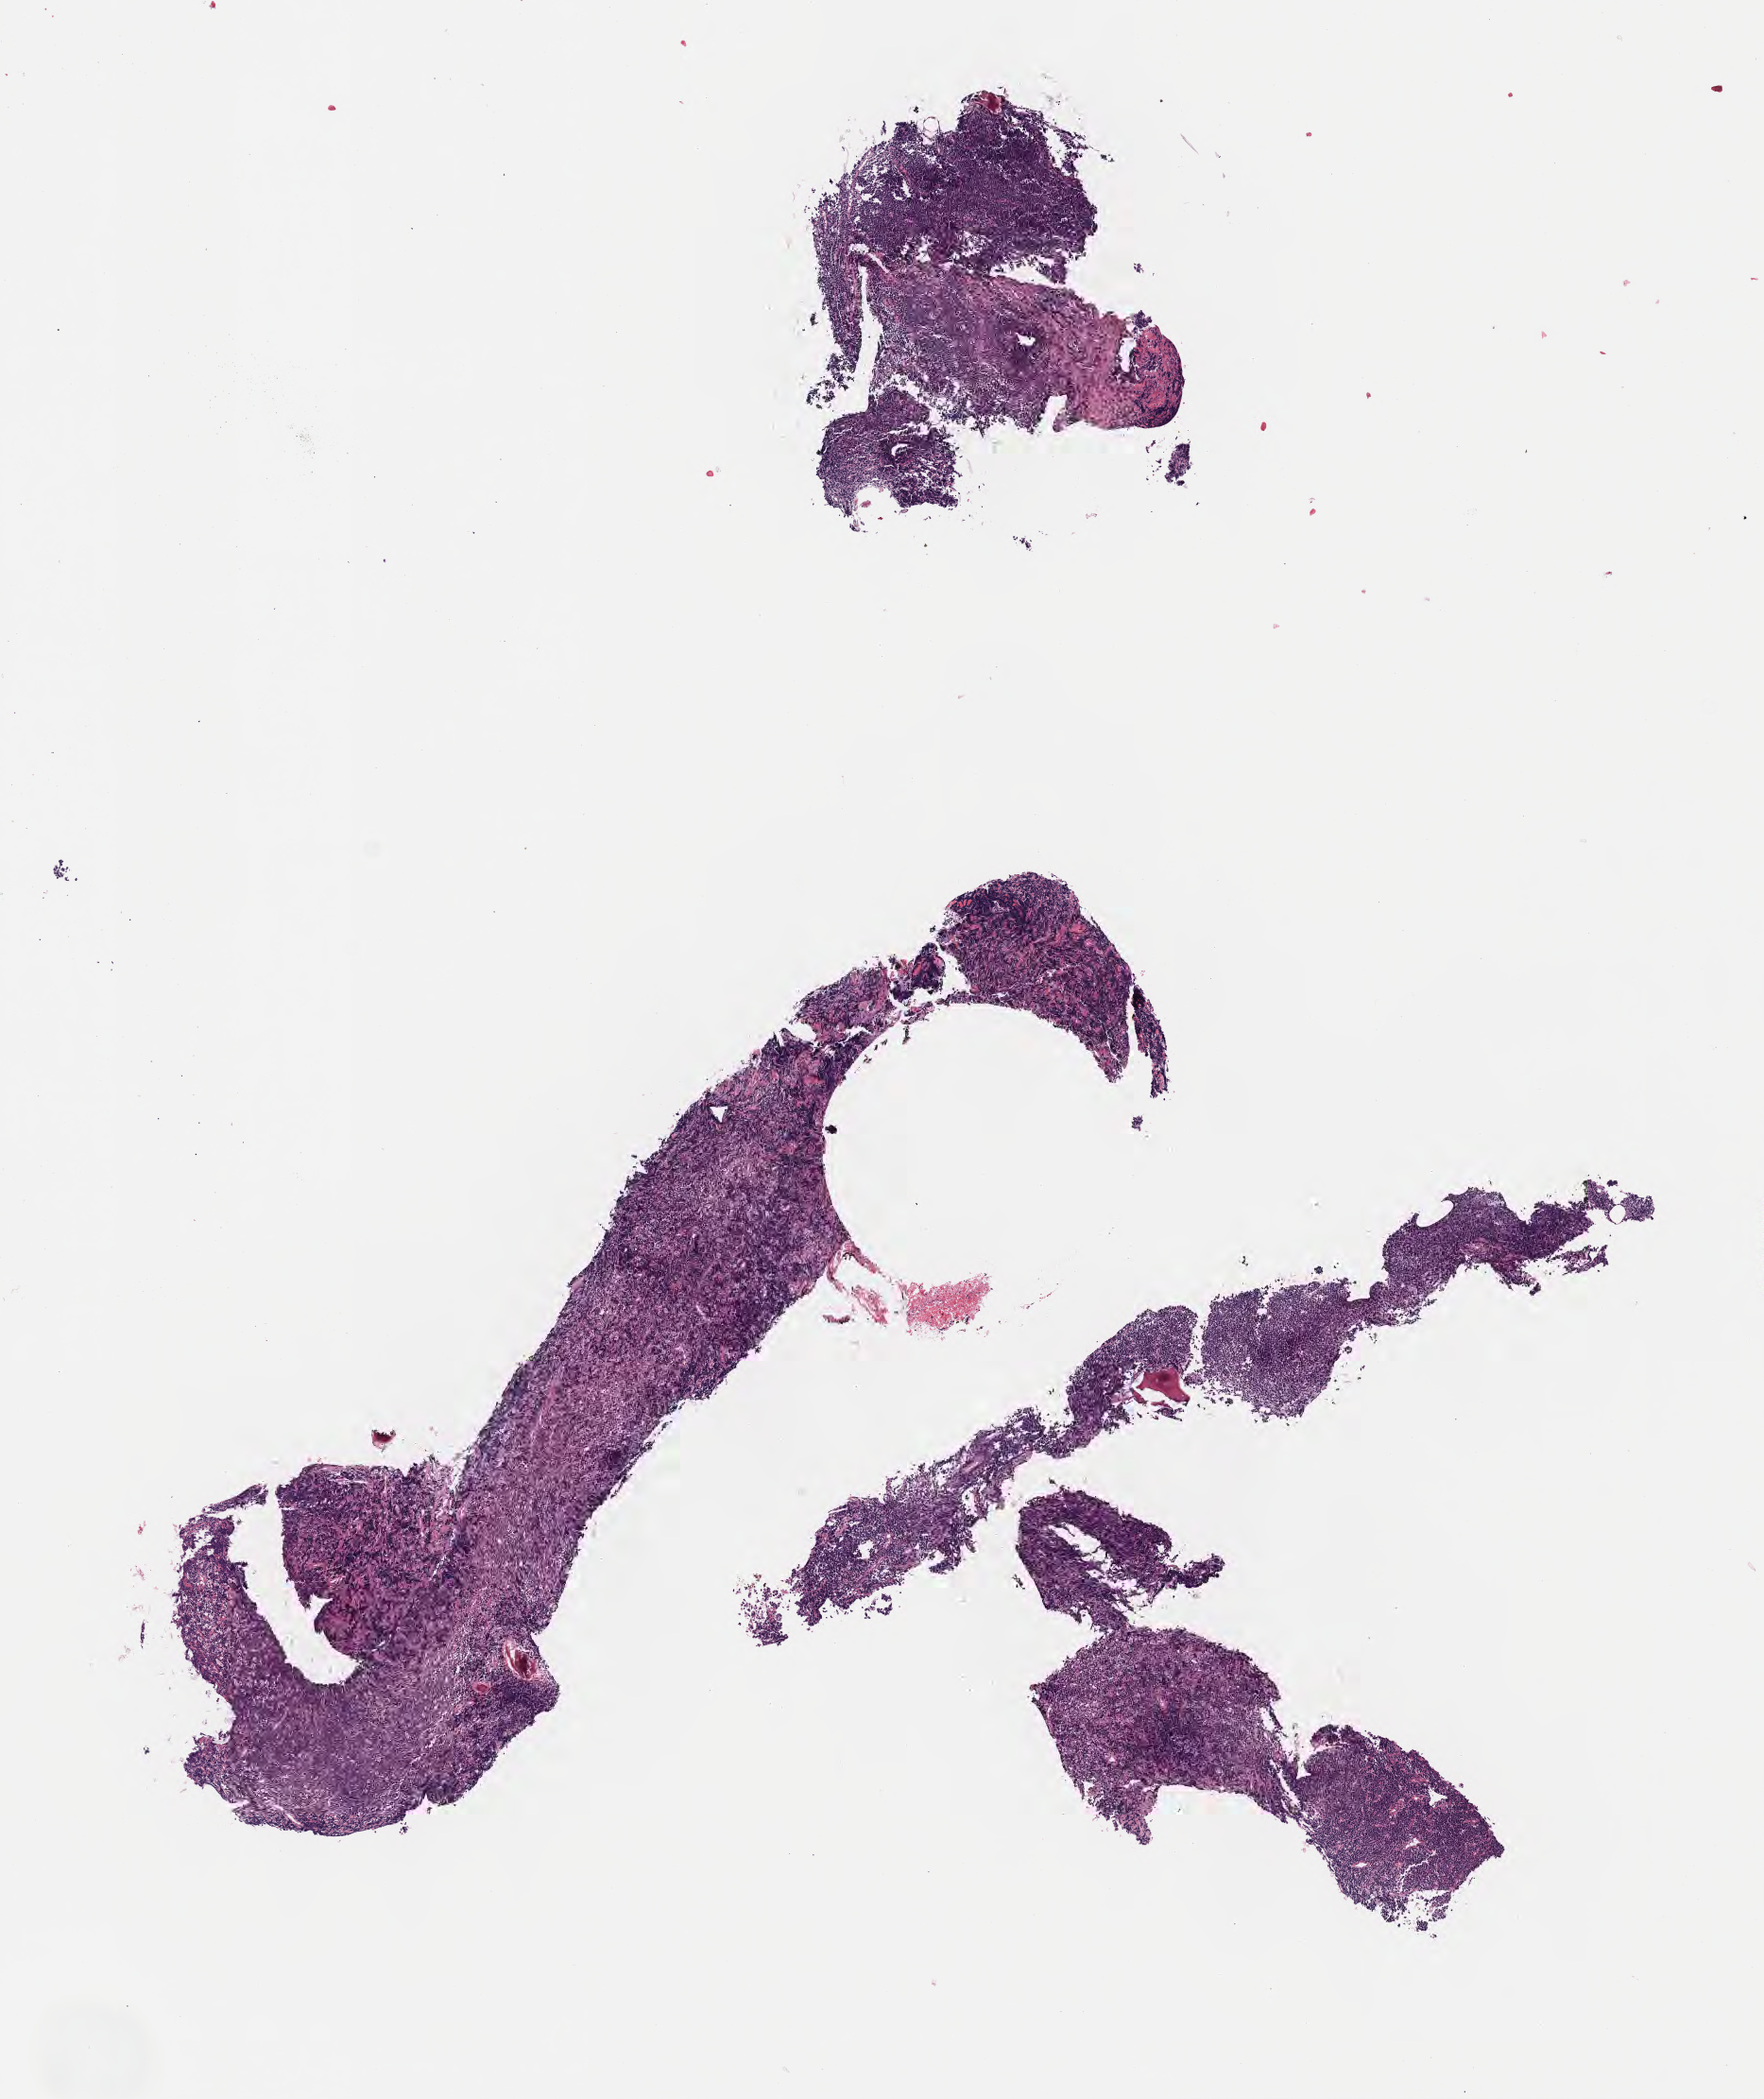
Haematoxylin and eosin whole-slide image — low-resolution overview of the scanned area, about 7.6 x 9.0 mm. Specimen: tumor tissue. Anatomic site: cranium. Patient: male, age at initial diagnosis 5 years.
Histologic diagnosis: Burkitt lymphoma, NOS.